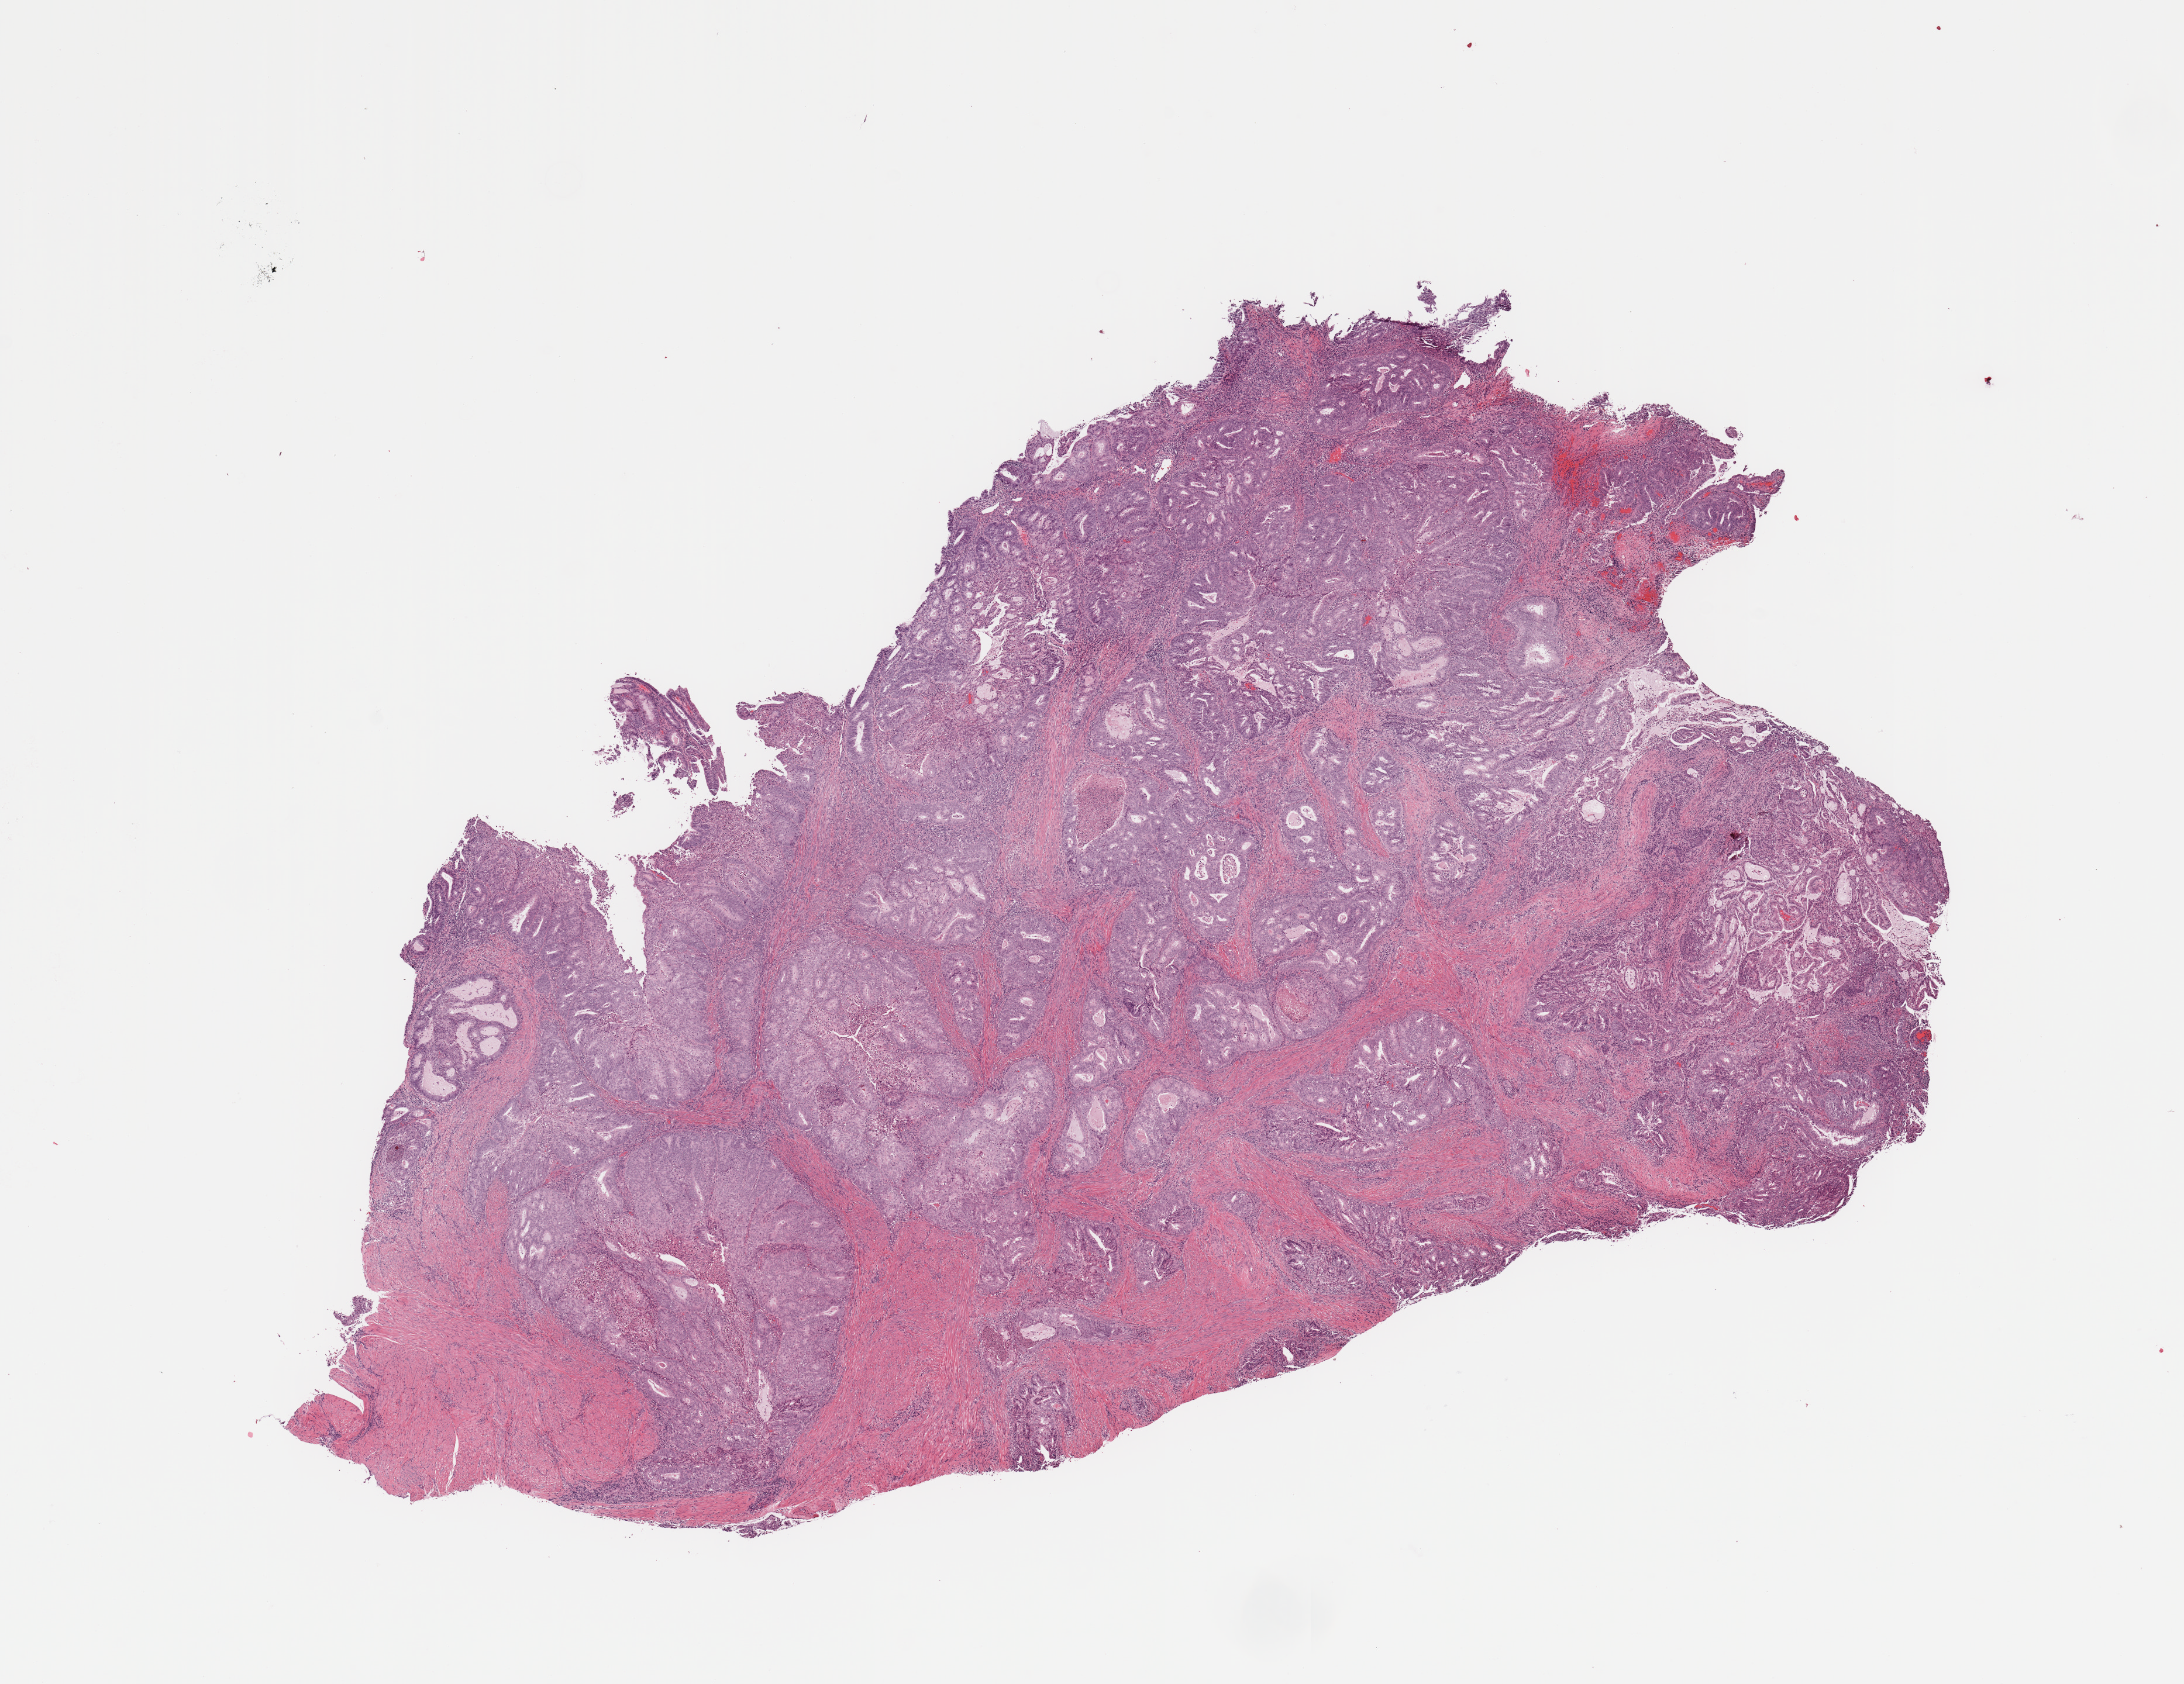
Hematoxylin and eosin (H&E) stained whole-slide image — whole scanned area (about 14.8 x 11.4 mm, slide scanned at 20x) shown as a low-resolution overview. Tumour tissue sample, sampled site: uterus. Patient: female, age 53 years. Pathologist review of this section (percent, as recorded): tumour nuclei 80%, necrosis 2%.
Diagnosis: Endometrioid adenocarcinoma, NOS.